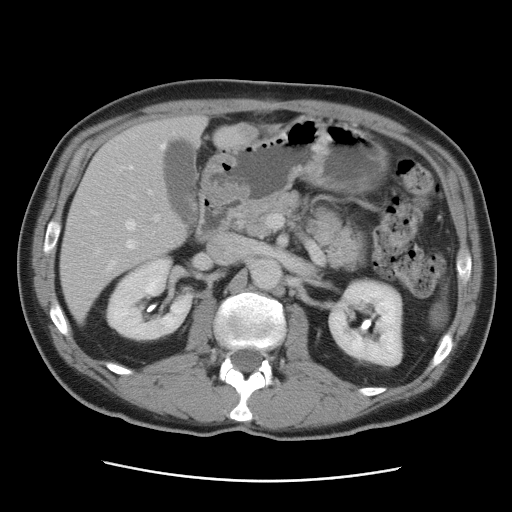
Contrast-enhanced abdominal CT, one axial slice; slice 45 of 89 in the series (ordered by position); 120 kVp; intravenous contrast given; soft-tissue window (W 400 / L 40 HU); 512 × 512 image matrix, field of view 366 × 366 mm. Male patient, age 59 years. Case-level facts recorded for this patient, not image findings: diagnosis: colorectal cancer liver metastases, imaged before liver resection; multiple liver metastases: yes; largest metastasis: 0.6 cm; chemotherapy before resection: no.
Outlined on this slice (expert manual segmentation):
- hepatic veins: bounding box <92,144,166,270> (left, top, right, bottom; pixels)
- liver: <61,117,259,324>
- planned liver remnant (the part of the liver to remain after resection): <71,117,204,245>
- portal vein (with intrahepatic branches): <132,190,159,221>
- liver metastasis: <237,126,256,140>